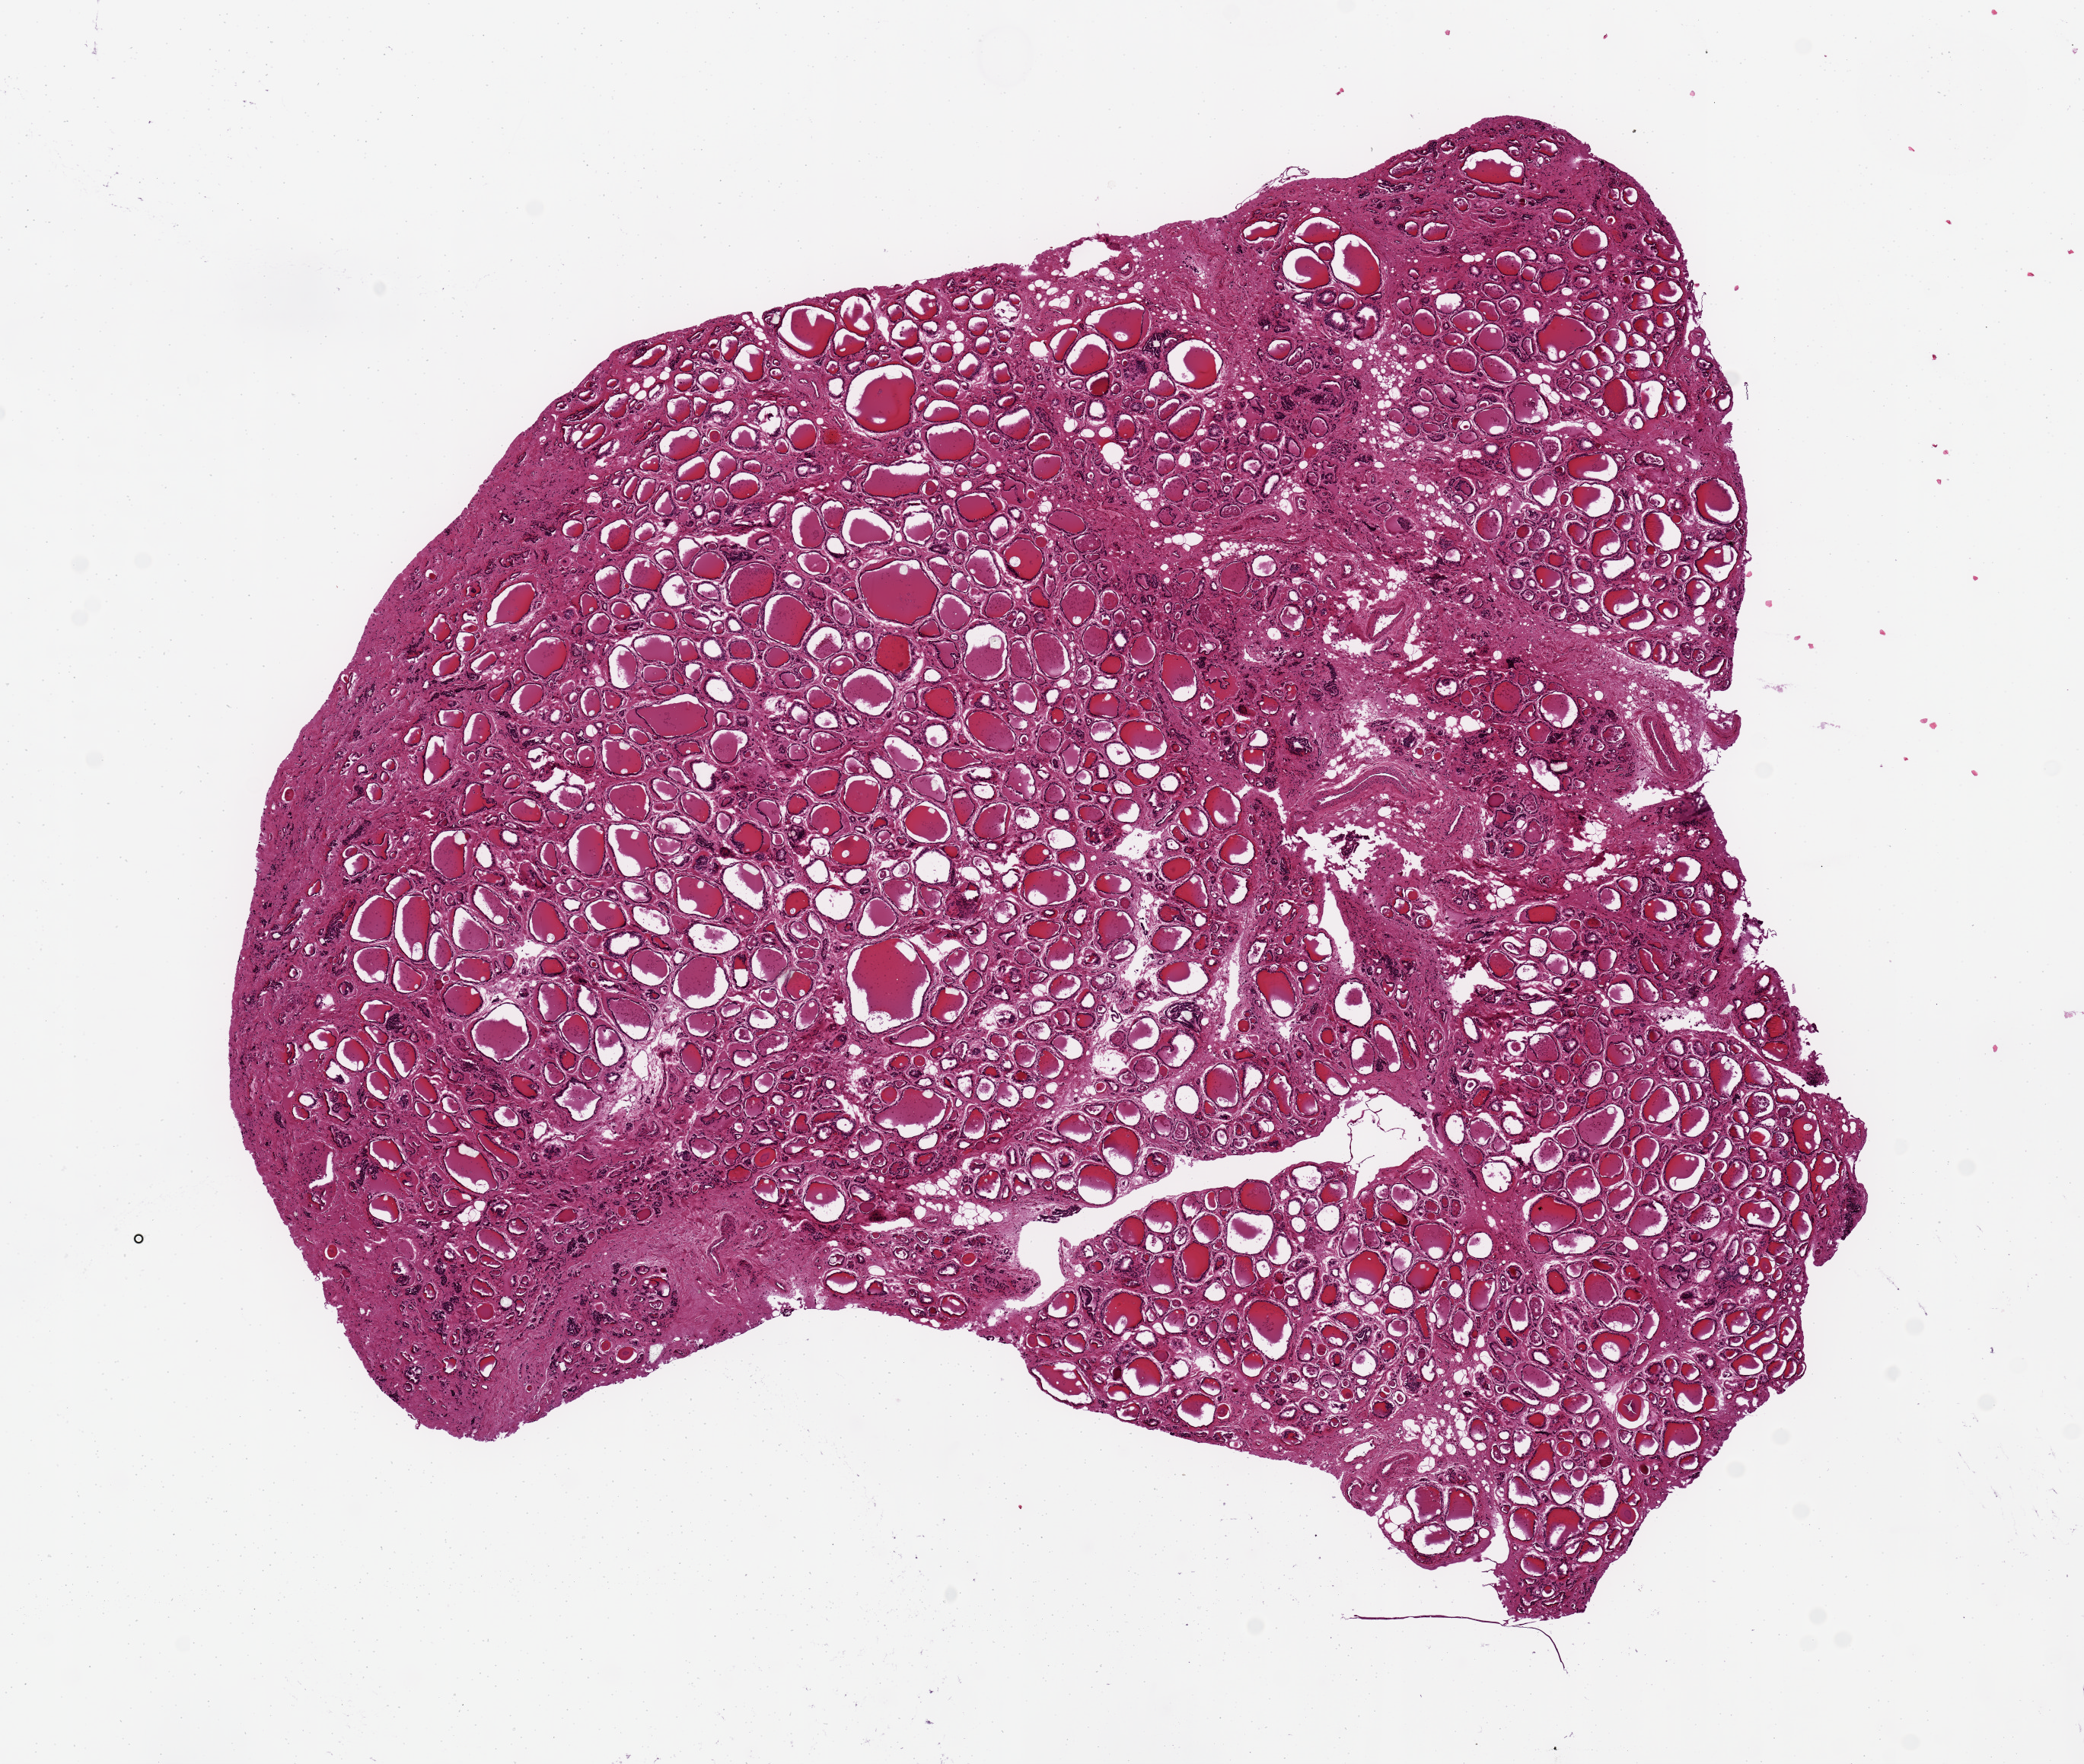
Whole-slide image, hematoxylin and eosin (H&E) stain, brightfield, low-resolution overview of the scanned area, about 10.8 x 9.2 mm; PAXgene-fixed paraffin-embedded (PFPE) section; sampled site (target tissue): thyroid; tissue donor sample. Donor sex: male.
• reviewer comment on this tissue sample: 9x8mm